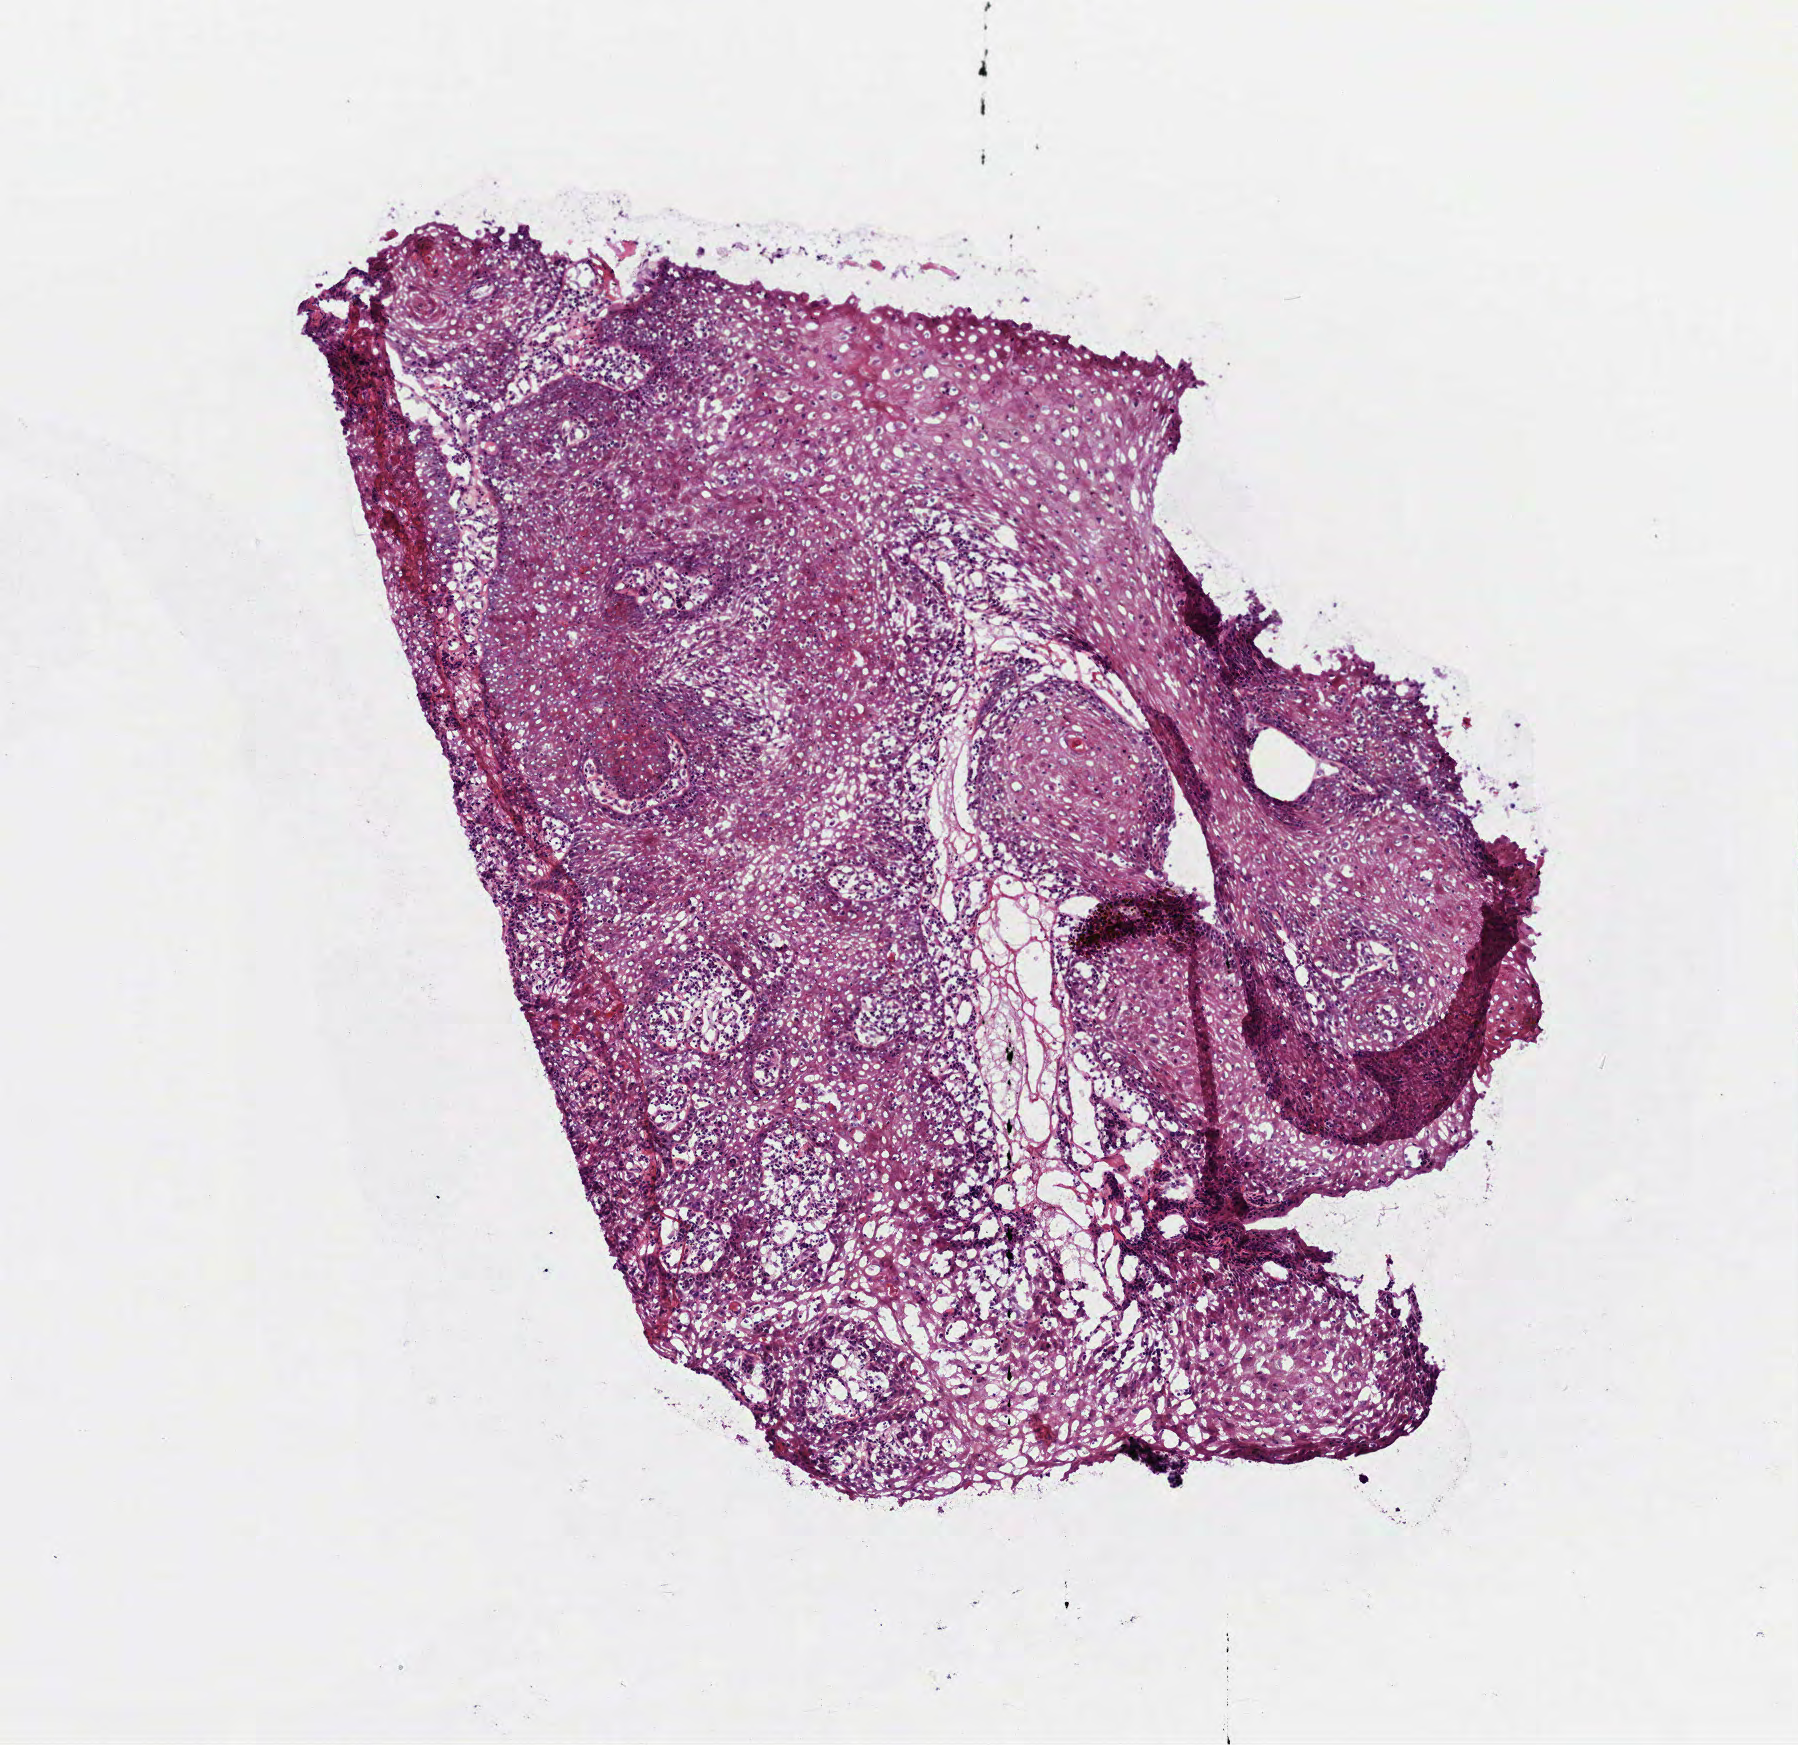
Hematoxylin and eosin (H&E) stained whole-slide image — whole scanned area (about 3.6 x 3.5 mm, slide scanned at 40x) shown as a low-resolution overview. Frozen section from the top of the tissue portion. Sample: primary tumour, head and neck. Female patient; age at initial diagnosis 59 years. Histologic grade: G1 (well differentiated). Slide review estimates, as recorded: tumour cells 90%, tumour nuclei 60%, normal cells 0%, stromal cells 10%, necrosis 0%. Inflammatory infiltration, as recorded: lymphocyte infiltration 38%, monocyte infiltration 0%, neutrophil infiltration 0%.
• AJCC pathologic stage: I
• histologic diagnosis: Squamous cell carcinoma, NOS (mouth, NOS)